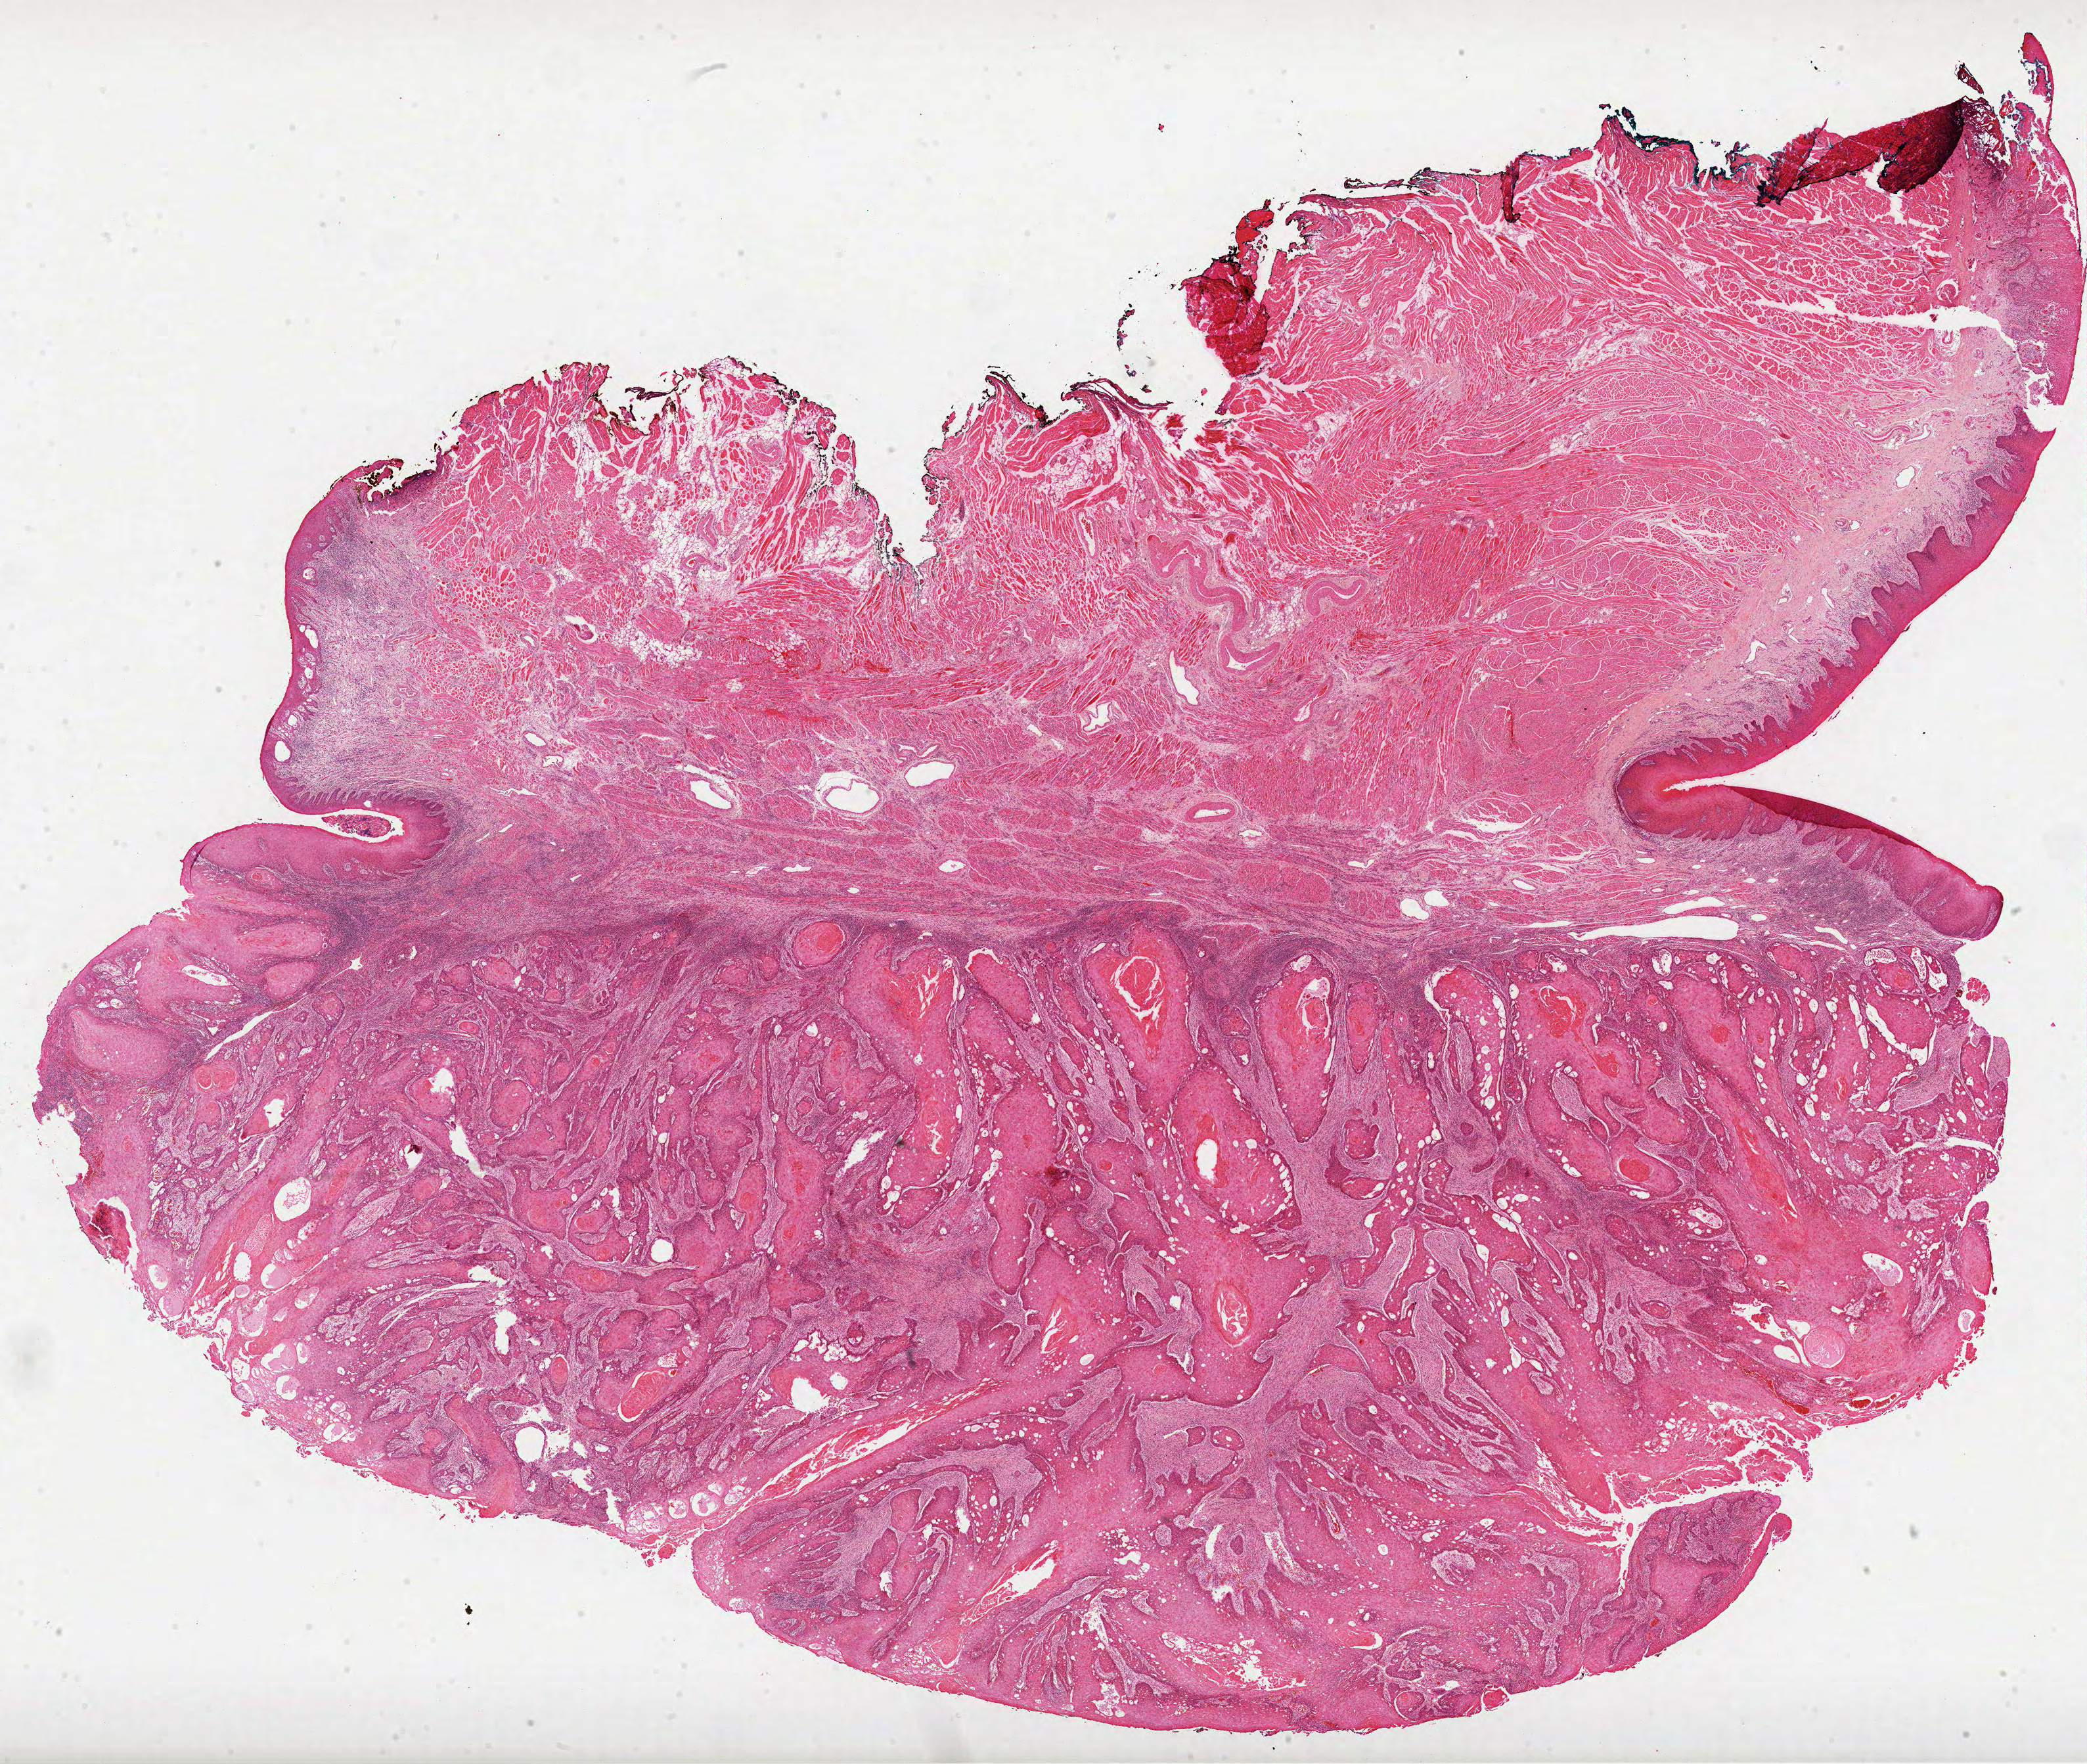
Digitized Hematoxylin and eosin (H&E) stained tissue section (whole slide) — a low-resolution overview of the entire scanned area, about 25.6 x 21.7 mm (from a 40x scan), formalin-fixed paraffin-embedded (FFPE) diagnostic section, sample: primary tumour, head and neck. Female, age 43 years at initial diagnosis. Histologic grade: G2 (moderately differentiated).
Histologic diagnosis: Squamous cell carcinoma, NOS (tongue, NOS). AJCC pathologic stage: III (7th edition).